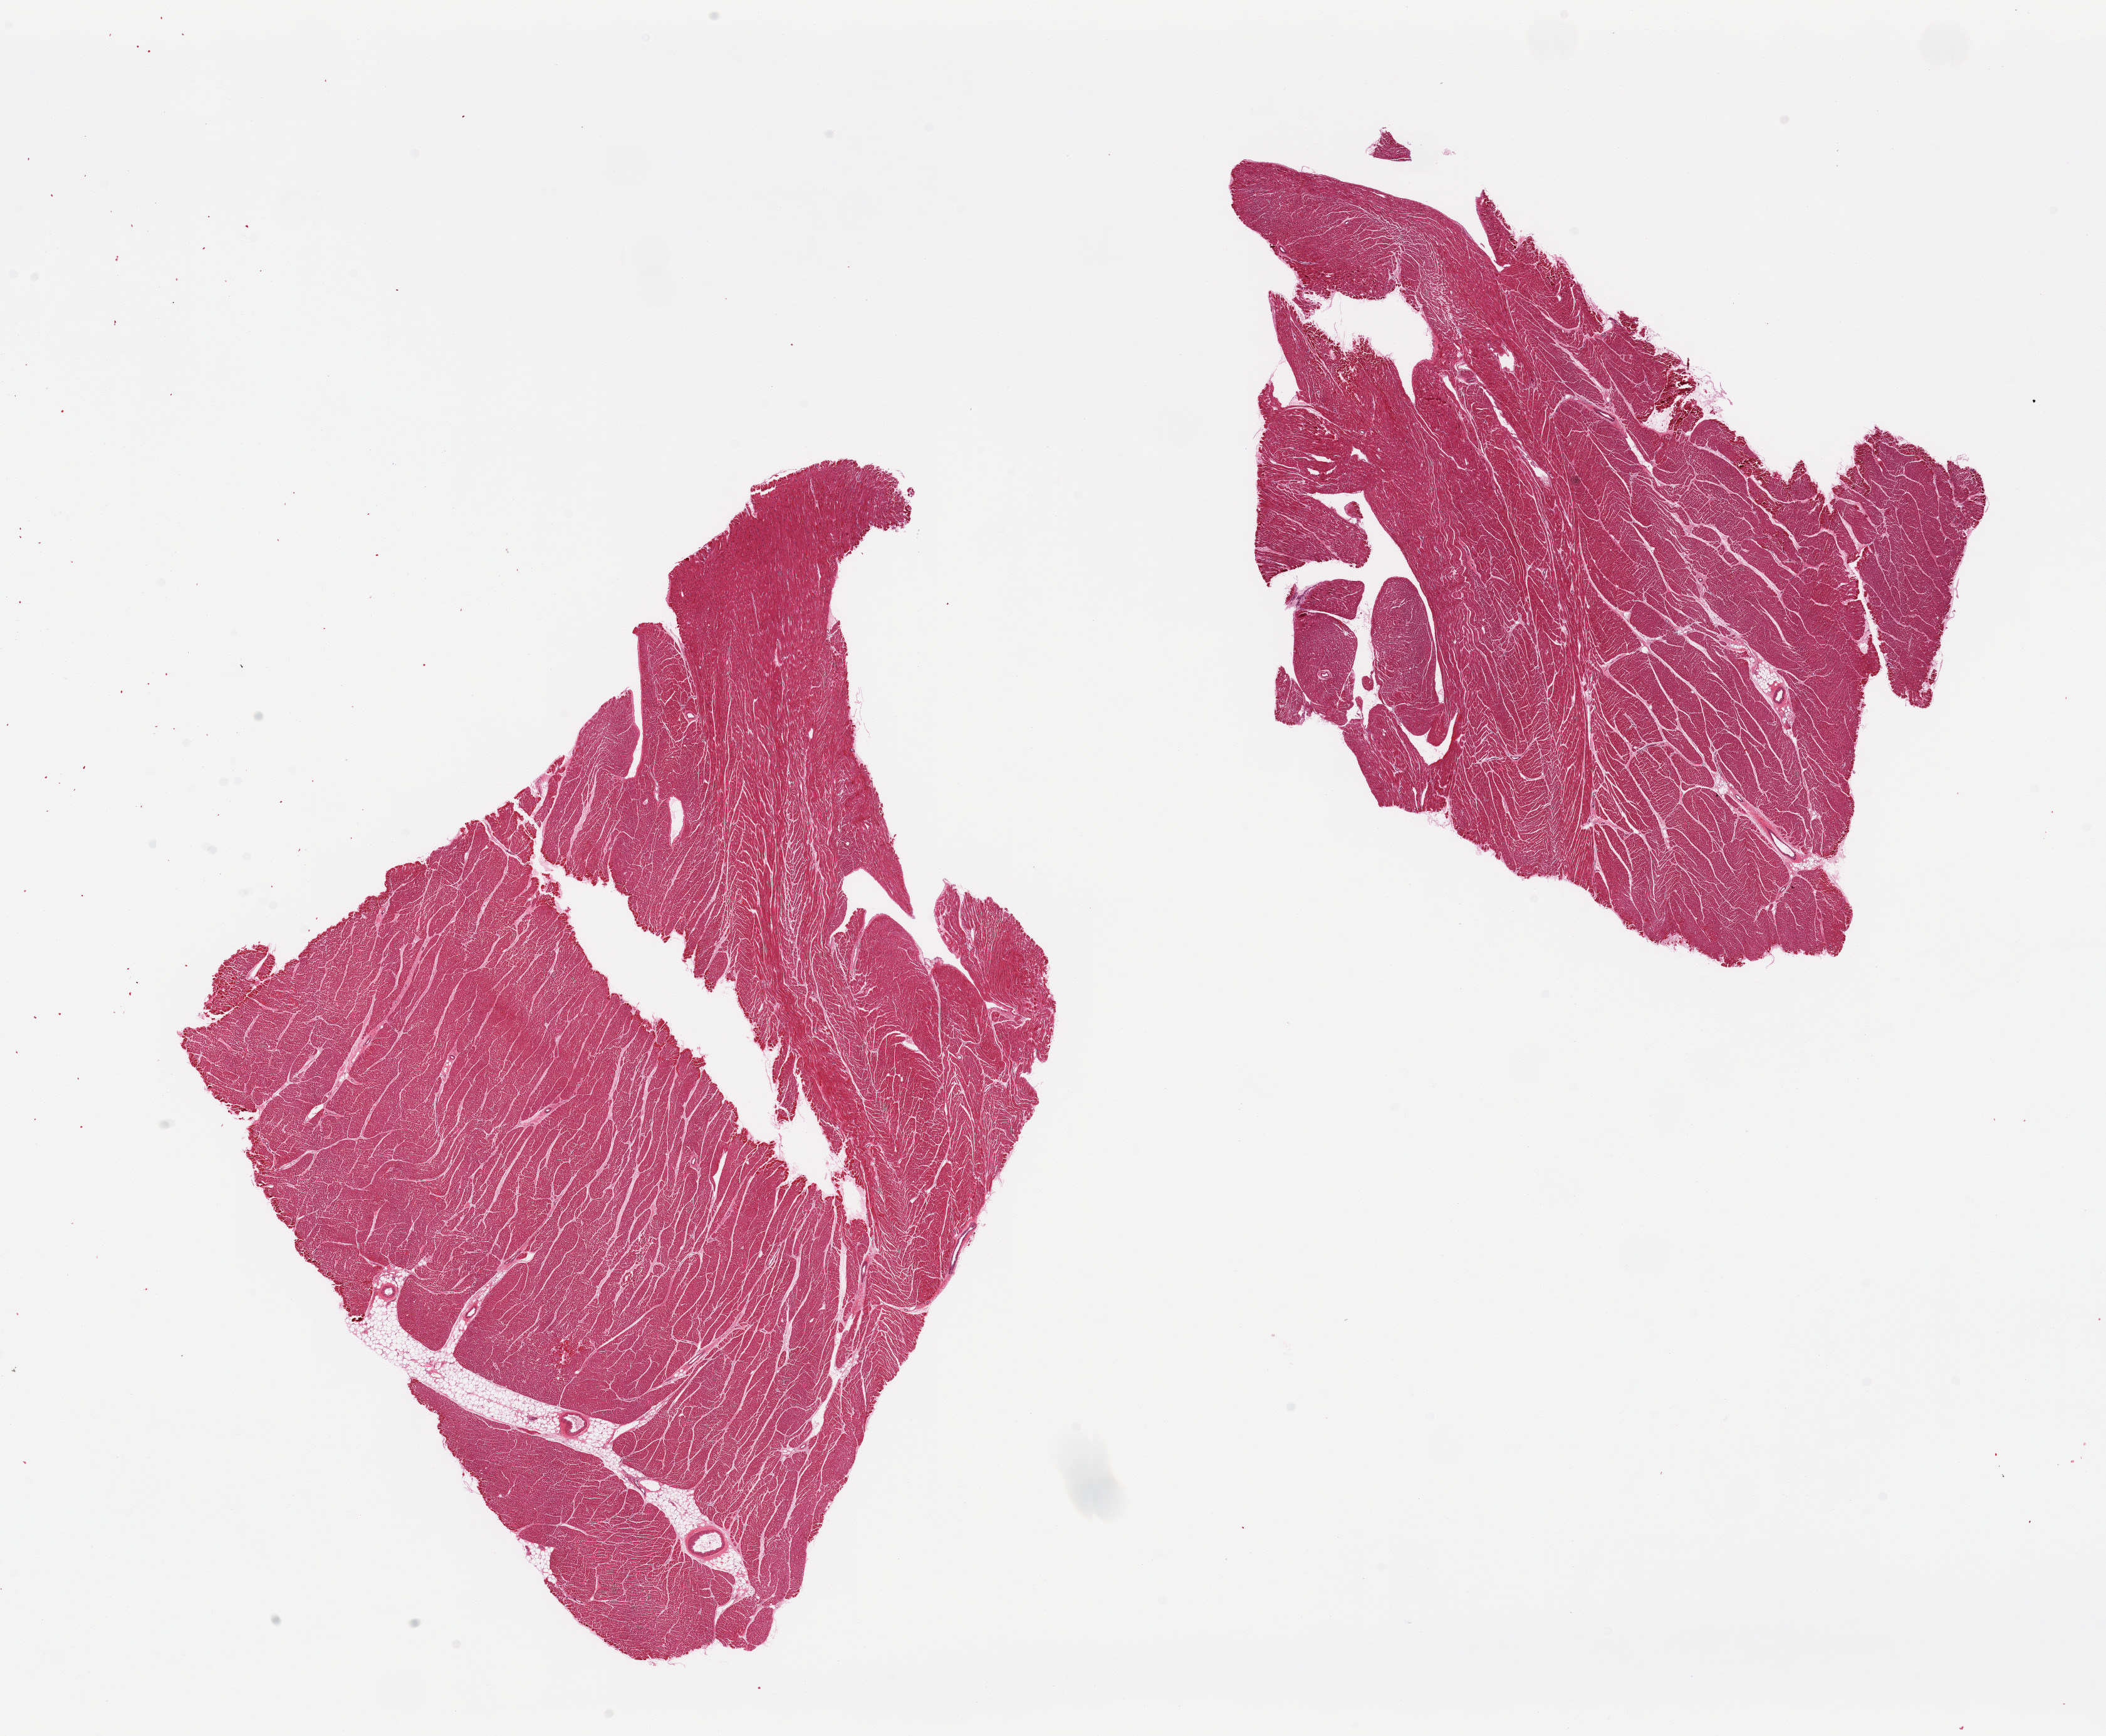
Digitized H&E-stained section, brightfield, whole scanned area (about 26.6 x 21.9 mm) shown as a low-resolution overview; PAXgene-fixed, paraffin-embedded tissue; section of heart (target tissue); tissue donor sample. Donor sex: male.
- reviewer comment on this tissue sample: 2 pieces